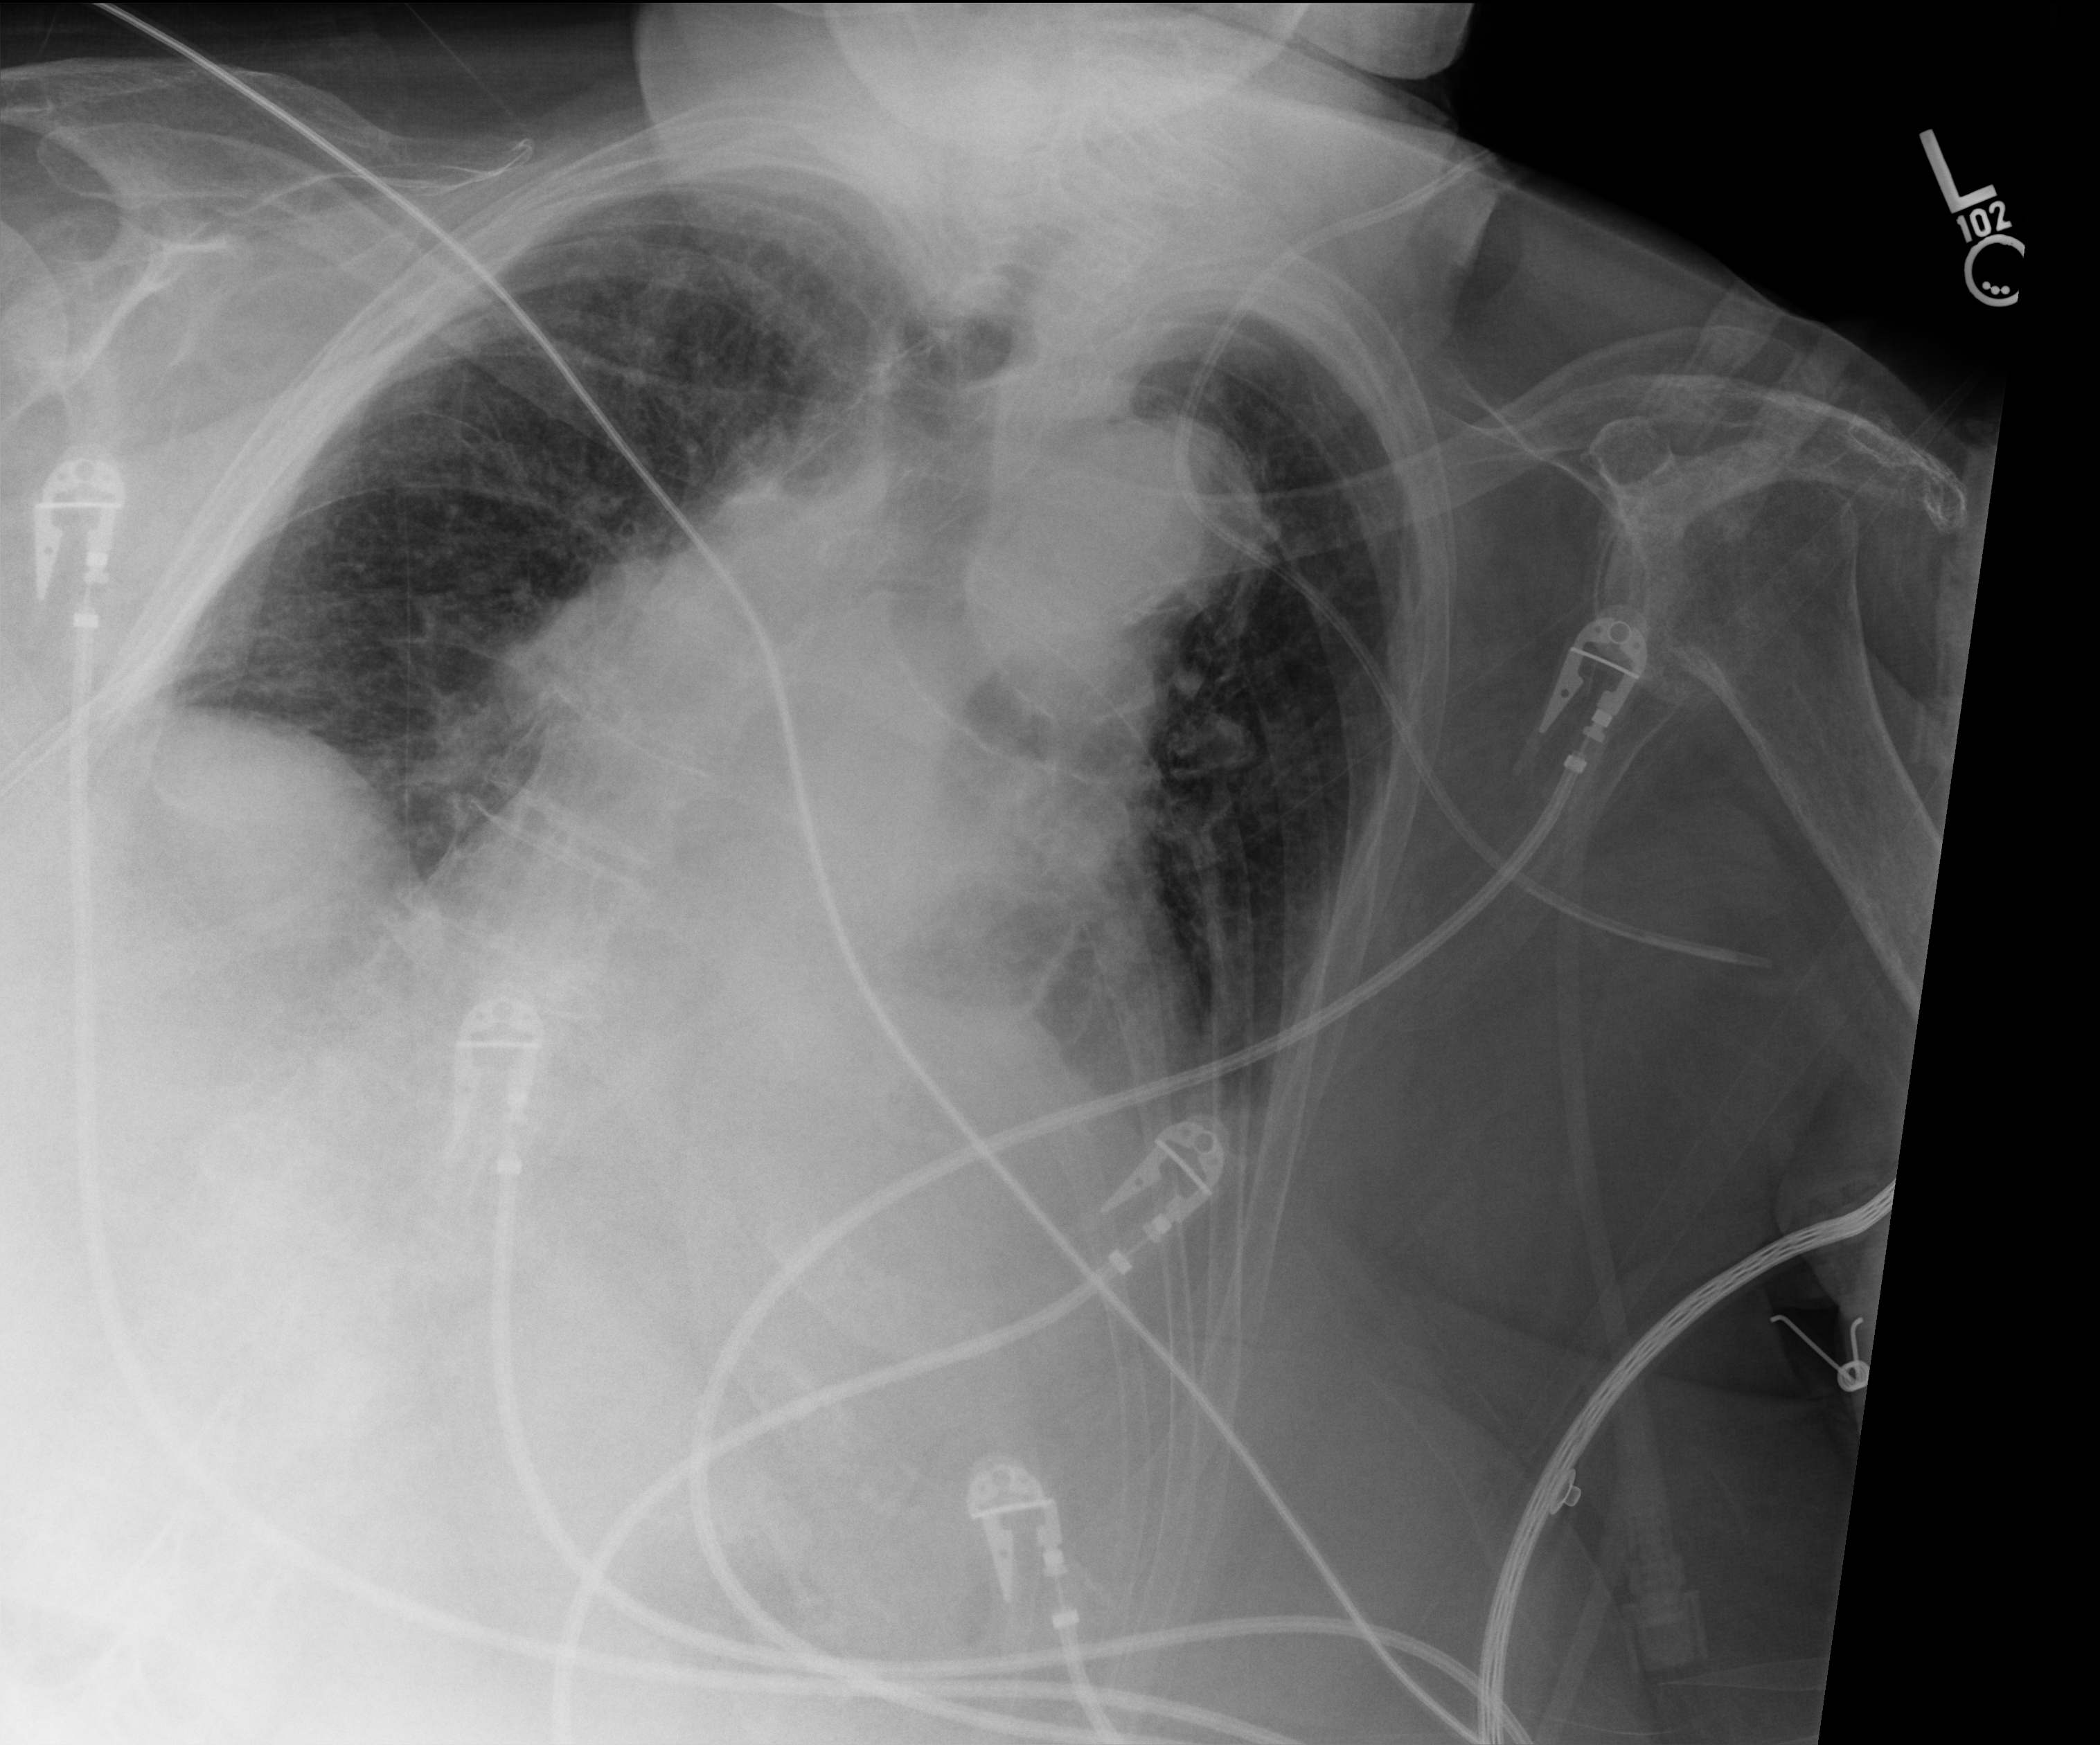
Chest X-ray (portable), anteroposterior (AP) projection. Female patient hospitalised with COVID-19, age 75–90 years.
Admission-level facts for this patient (not findings on this image; timing relative to this image not recorded): admitted to intensive care during this hospital stay: yes; length of hospital stay: 12 days; mechanically ventilated during this hospital stay: no.